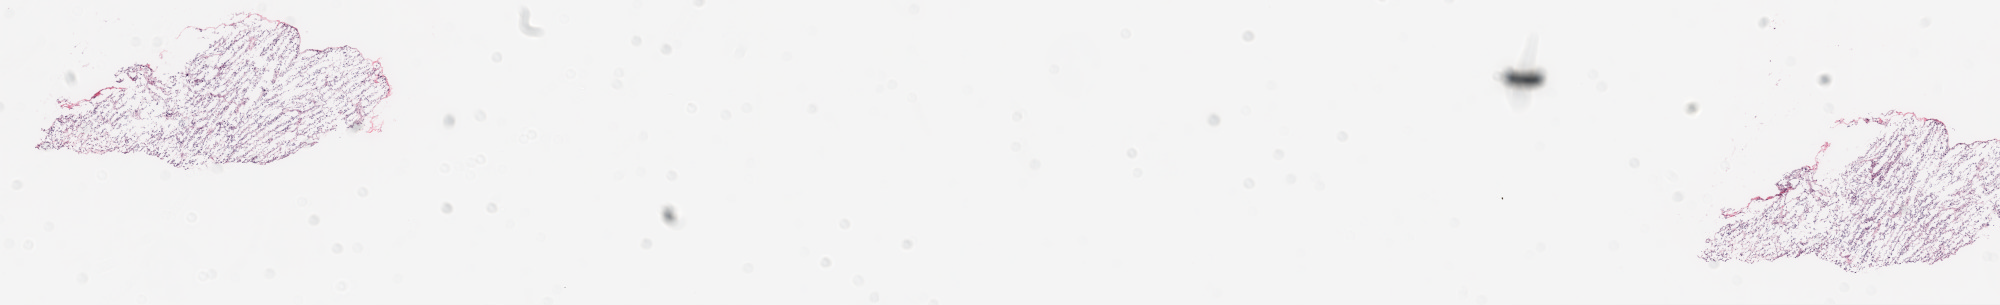
Whole-slide histology image, H&E — whole scanned area (about 16.0 x 2.4 mm, slide scanned at 20x) shown as a low-resolution overview, frozen section from the top of the tissue portion, sample: primary tumour, brain. Patient: female, age at initial diagnosis 48 years. Composition of this section per pathologist review: tumour cells 95%, tumour nuclei 95%, normal cells 0%, stromal cells 5%, necrosis 0%.
Histologic diagnosis: Glioblastoma.